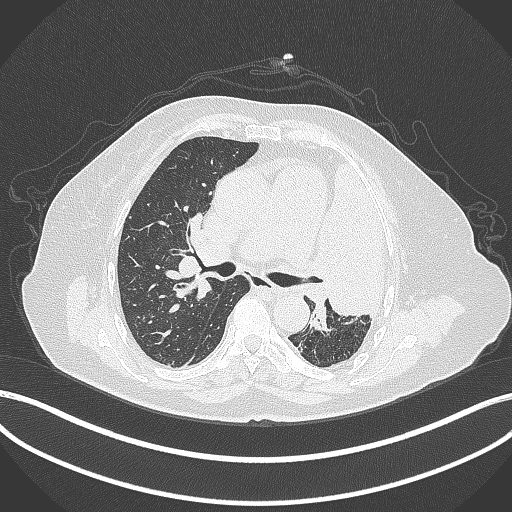
Chest CT, one axial slice; position 235 of 399 along the scan axis; 120 kVp; lung window (W 1500 / L -600 HU); 1 mm slice thickness; 512 × 512 image matrix, field of view 400 × 400 mm. Female patient, age 75 years. From the clinical record (not read from this slice): clinical TNM (as recorded): T3 N3 M1.
Outlined on this slice (bounding box drawn by a radiologist):
- lung tumour (recorded histology: adenocarcinoma): bounding box <306,154,390,318> (left, top, right, bottom; pixels)